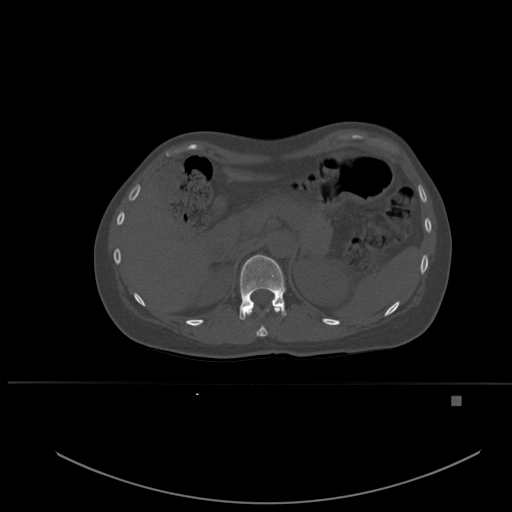
CT including the spine, one axial slice. Position 260 of 651 along the scan axis. Bone window (W 1800 / L 400 HU). 512 × 512 image matrix, field of view 443 × 443 mm. Patient: female, 49 years. From the clinical record (not read from this slice): primary cancer: breast.
Structures marked on this image (semi-automatically segmented with operator editing):
- T11 vertebra: box from (x=246, y=307) to (x=285, y=337) px
- T12 vertebra: (x=239, y=255)–(x=287, y=320)